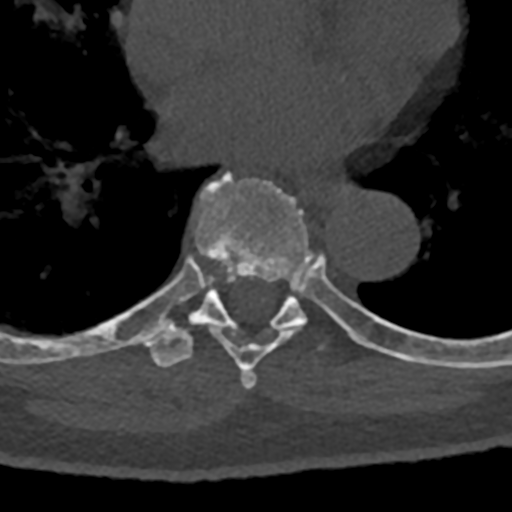
CT including the spine, one axial slice. Position 738 of 797 along the scan axis. Reconstruction kernel Br40s/3. 120 kVp. Bone window (W 1800 / L 400 HU). 0.5 mm slice thickness. 512 × 512 image matrix, field of view 160 × 160 mm. Patient: male, 74 years. Case-level facts recorded for this patient, not image findings: primary cancer: renal; vertebrae with lytic lesions (as recorded): T10, L1, L2, L3, L4, L5.
Annotated regions visible in this slice (semi-automatically segmented with operator editing):
- T7 vertebra: bounding box <187,171,370,389> (left, top, right, bottom; pixels)
- T8 vertebra: <70,274,432,368>